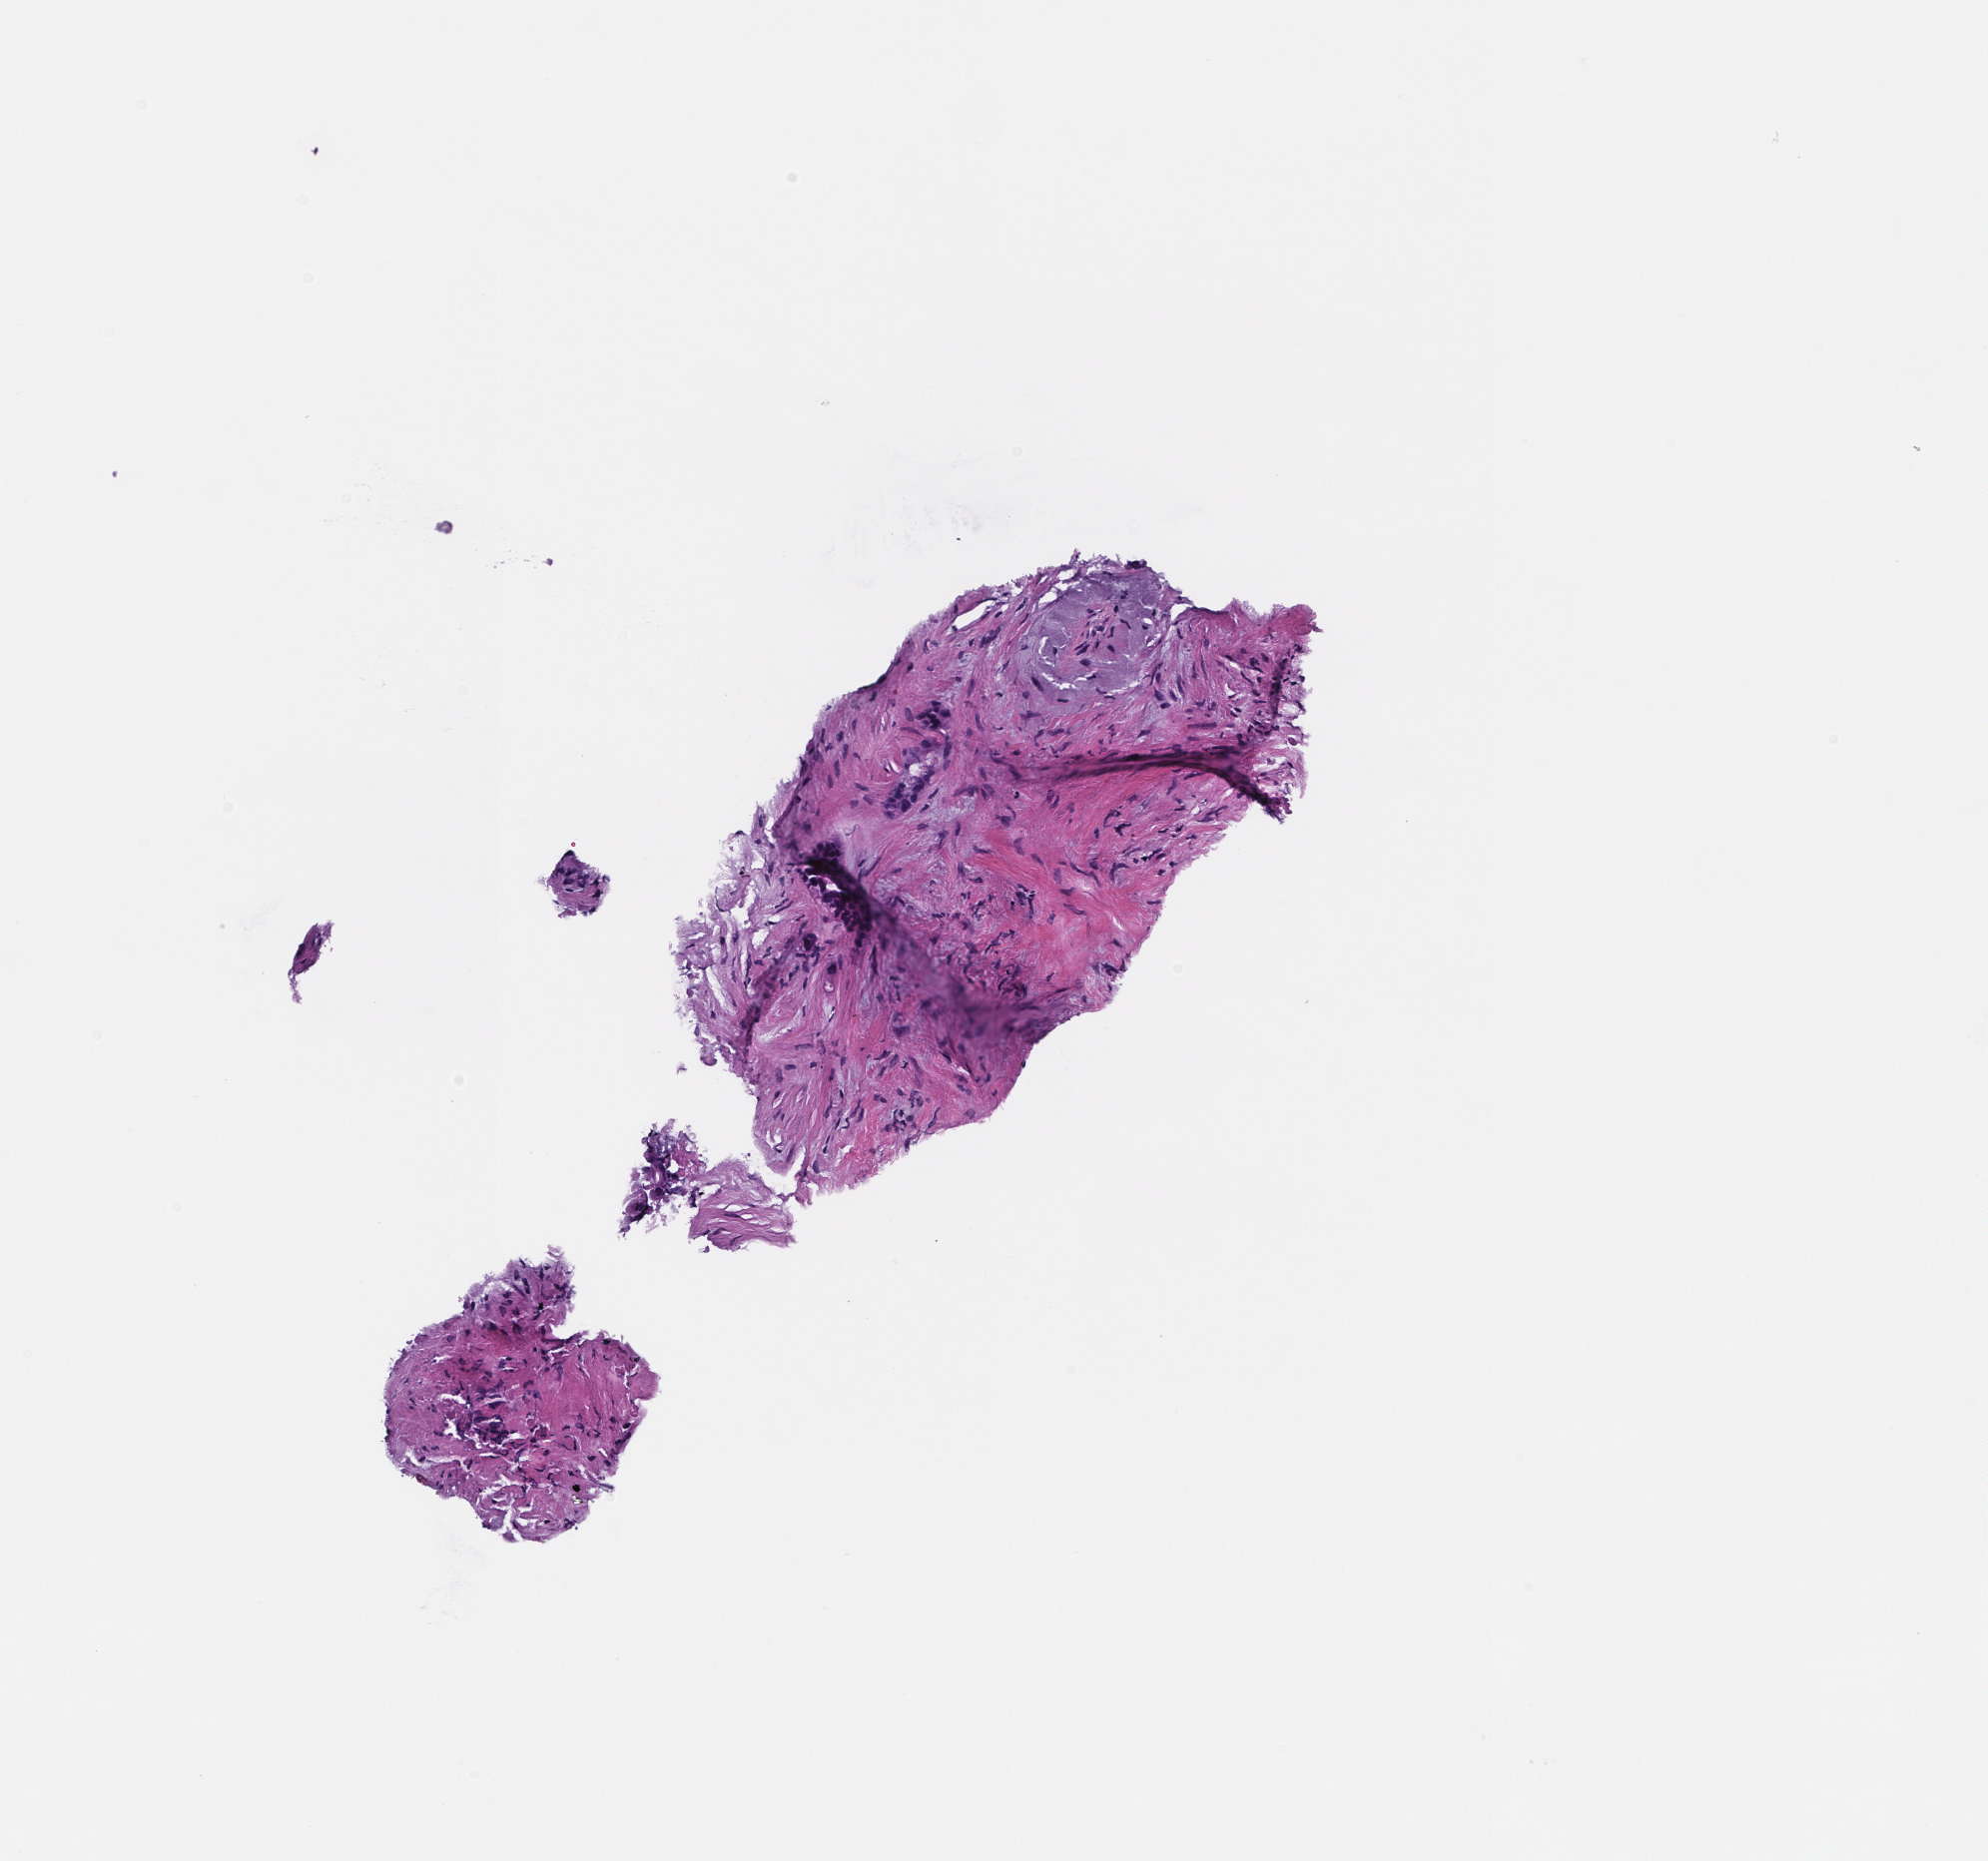
Digitized hematoxylin and eosin (H&E)-stained section, shown as a low-resolution overview of the whole scanned area (about 2.0 x 1.9 mm); FFPE section; collected at baseline (before treatment). Patient sex: male.
* this section: metastatic tumor tissue
* primary diagnosis of the patient: Colorectal Carcinoma